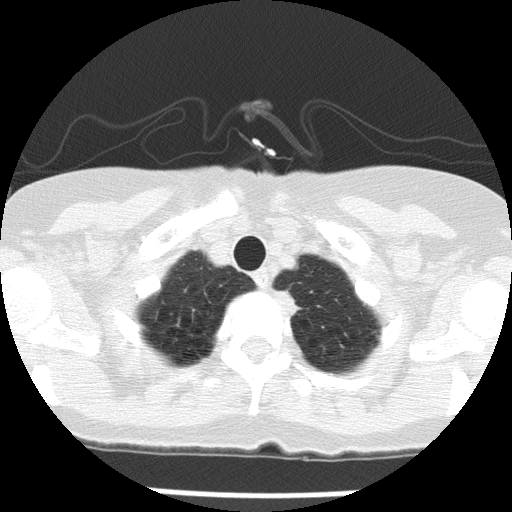
Low-dose screening chest CT, axial slice. Baseline screening round. Lung window (W 1500 / L -600 HU). 2 mm slice thickness. Lung (sharp) reconstruction kernel (FC51). Slice 14 of 143 in the series. Female, age 74 years at enrolment. Former smoker at enrolment.
- Expert reader's lesion annotation, bounding box <267,287,306,320> (left, top, right, bottom; pixels).
- The screening reader recorded 2 non-calcified nodules or masses ≥4 mm on this exam (left lower lobe, left upper lobe); which of them this box marks is not recorded.
- Official screen result: positive, change unspecified: nodule(s) >= 4 mm or enlarging nodule(s), mass(es), or other non-specific abnormalities suspicious for lung cancer.
- Lung cancer was diagnosed 81 days after this screen: adenocarcinoma, NOS, left upper lobe, poorly differentiated (G3), stage IA (AJCC 6th edition), 24 mm at pathology.